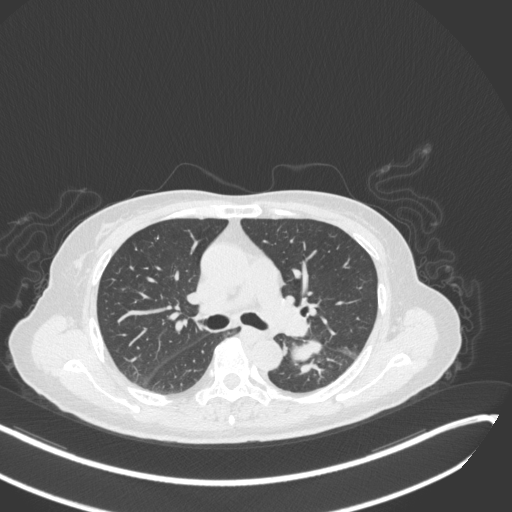
Chest CT, one axial slice. Position 176 of 342 along the scan axis. Reconstruction kernel B31f. Lung window (W 1500 / L -600 HU). 1 mm slice thickness. 512 × 512 image matrix, field of view 400 × 400 mm. Female patient, age 64 years. Case-level facts recorded for this patient, not image findings: clinical TNM (as recorded): T3 N1 M1; histopathological grade: G3.
Structures marked on this image (rectangle marked by the reading radiologist):
- lung tumour (recorded histology: small cell carcinoma): bounding box <285,332,327,365> (left, top, right, bottom; pixels)